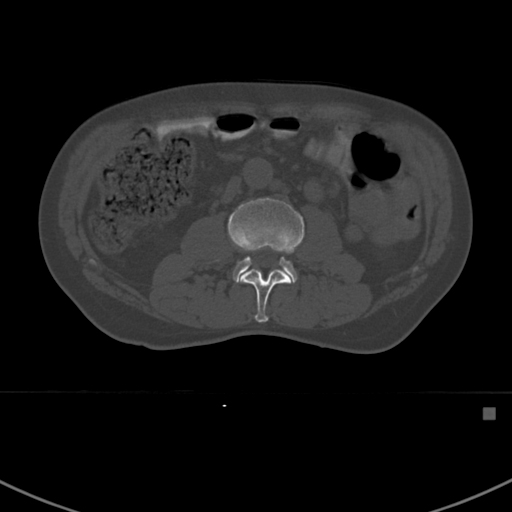
CT including the spine, one axial slice; position 275 of 412 along the scan axis; reconstruction kernel Br40s; bone window (W 1800 / L 400 HU); 1.5 mm slice thickness; 512 × 512 image matrix, field of view 358 × 358 mm. Patient: male, 59 years. Case-level facts recorded for this patient, not image findings: primary cancer: prostate.
Structures marked on this image (semi-automatically segmented with operator editing):
- L2 vertebra: bounding box <240,269,292,323> (left, top, right, bottom; pixels)
- L3 vertebra: <228,197,305,283>